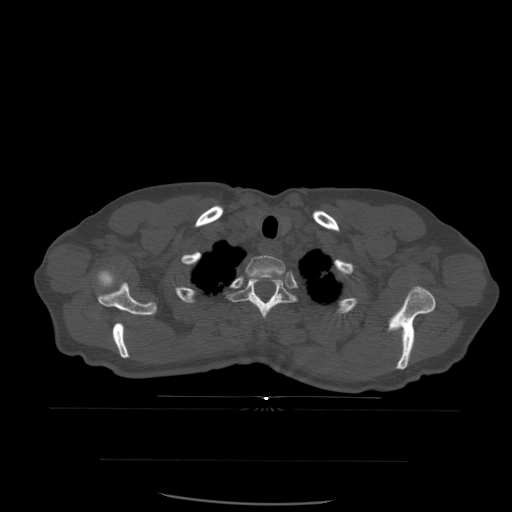
CT including the spine, one axial slice. Bone window (W 1800 / L 400 HU). 512 × 512 image matrix, field of view 392 × 392 mm. Patient age 48 years. Case-level facts recorded for this patient, not image findings: primary cancer: lung; vertebrae with lytic lesions (as recorded): T11.
Structures marked on this image (semi-automatically segmented with operator editing):
- T1 vertebra: box from (x=248, y=255) to (x=286, y=295) px
- T2 vertebra: (x=227, y=273)–(x=297, y=321)